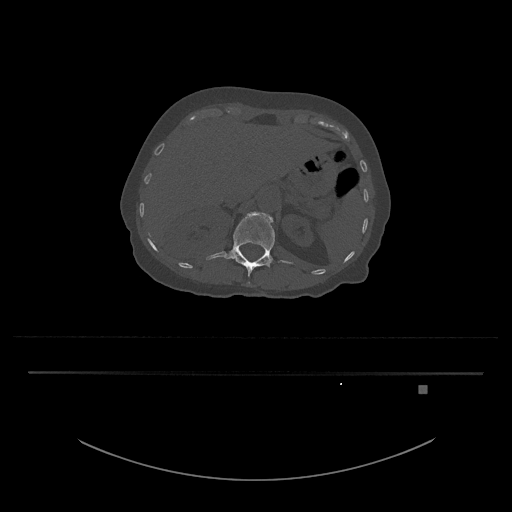
CT including the spine, one axial slice. Position 552 of 797 along the scan axis. Reconstruction kernel Br40s/3. 120 kVp. Bone window (W 1800 / L 400 HU). 0.5 mm slice thickness. 512 × 512 image matrix, field of view 500 × 500 mm. Patient: female, 57 years. Case-level facts recorded for this patient, not image findings: primary cancer: cervical.
Outlined on this slice (semi-automatic segmentation, software-assisted and operator-edited):
- L1 vertebra: bounding box <206,212,294,284> (left, top, right, bottom; pixels)